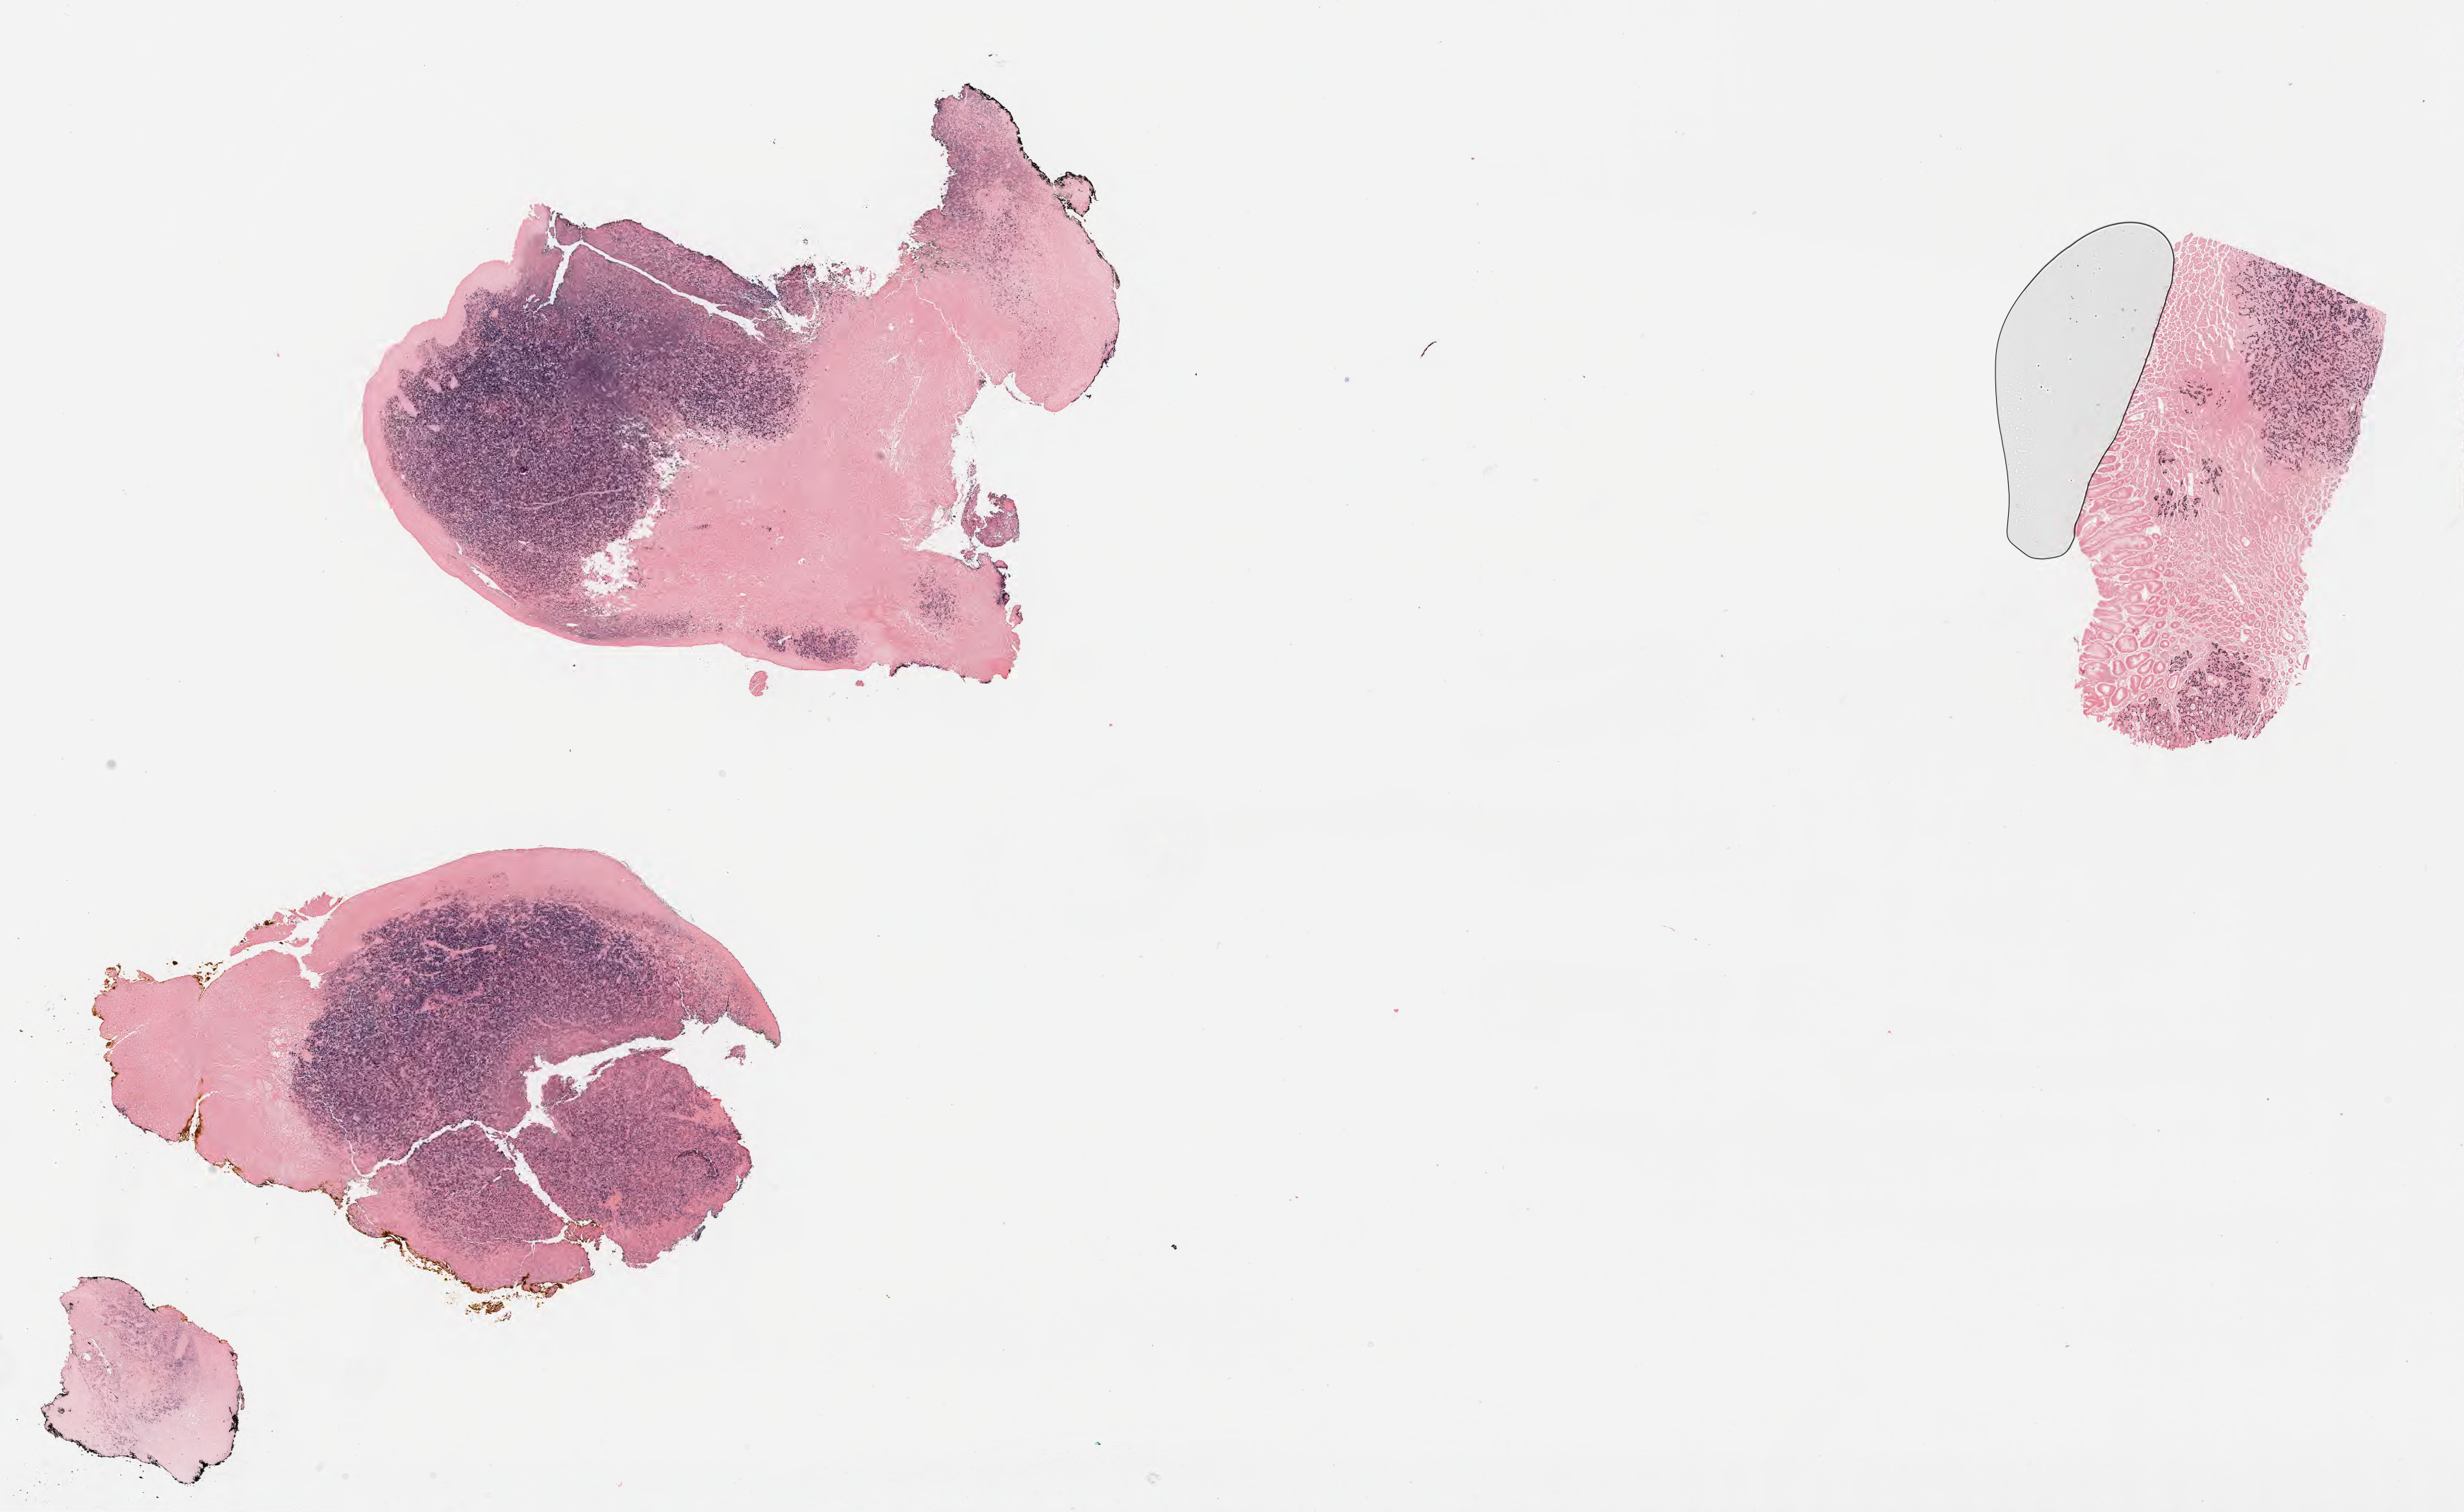
Whole-slide image, Epstein–Barr virus-encoded RNA (EBER) in-situ hybridisation — shown as a low-resolution overview of the whole scanned area (about 28.2 x 17.3 mm); specimen: tumor tissue. Patient: male, age 49 years.
* diagnosis: Diffuse large B-cell lymphoma, NOS